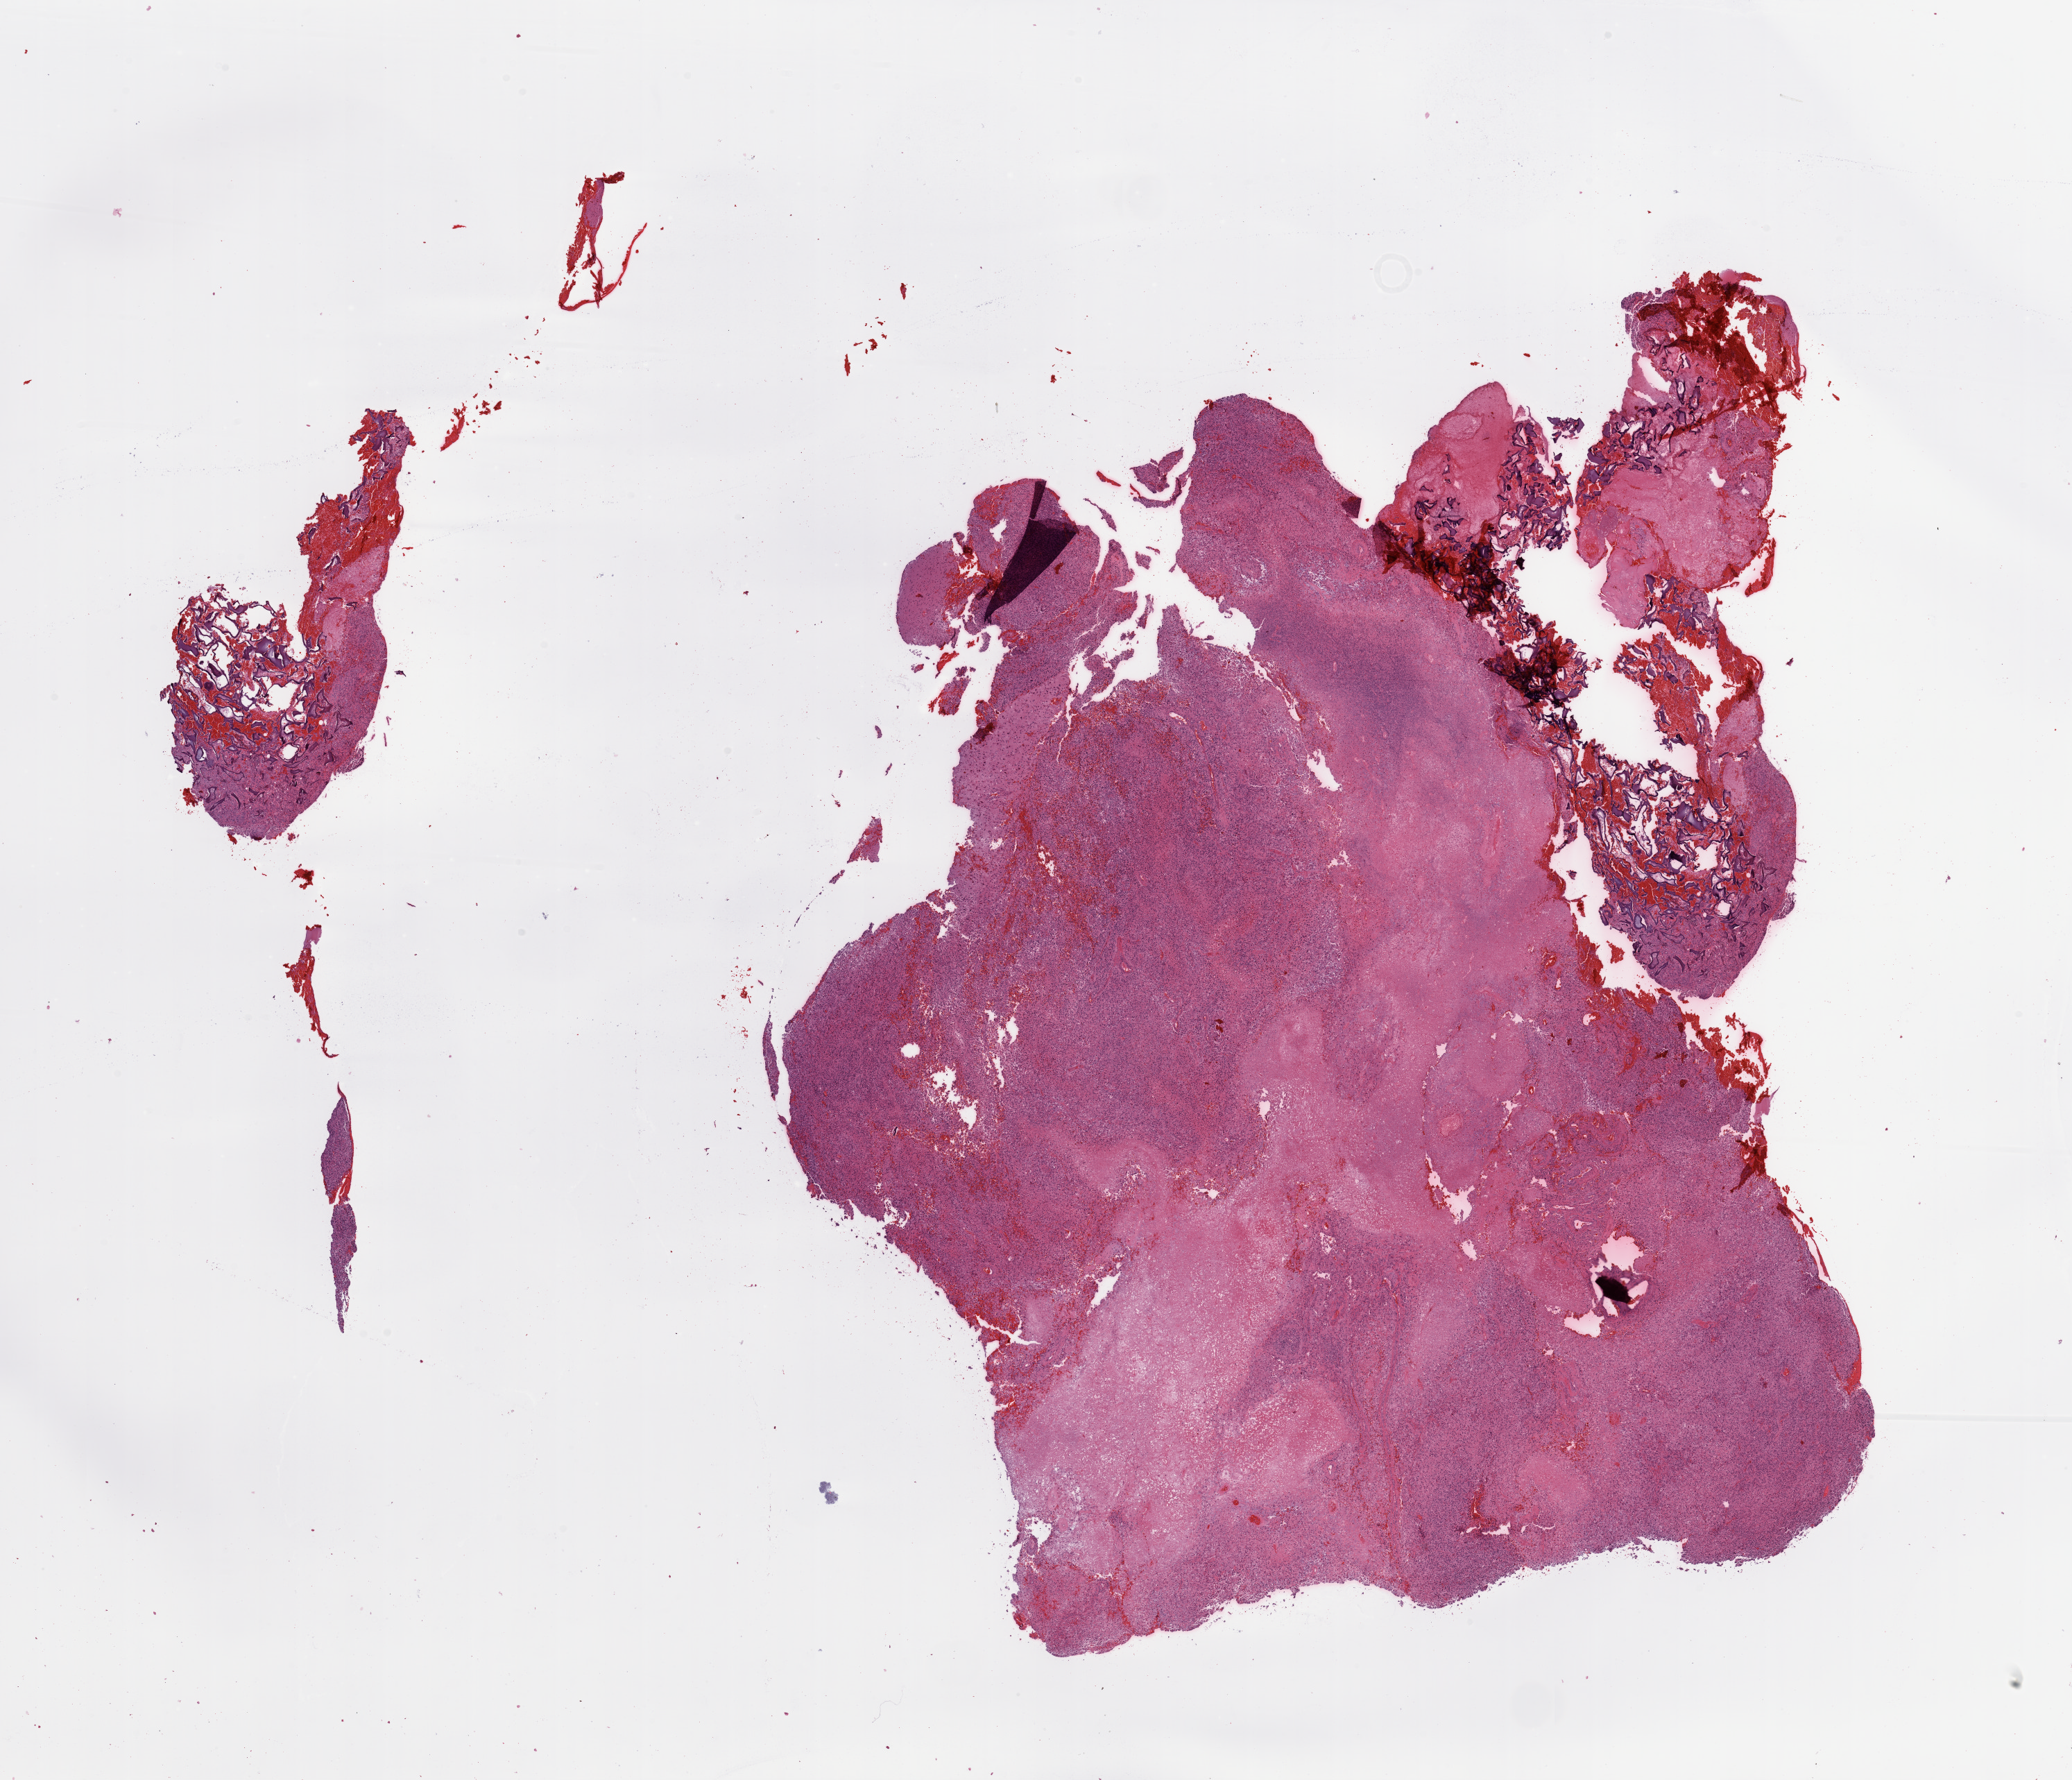
Hematoxylin and eosin (H&E) stained whole-slide image, low-resolution overview of the scanned area, about 23.6 x 20.3 mm (slide scanned at 20x), tumour tissue sample, sampled site: frontal lobe. Male, 60 y/o. Slide review estimates, as recorded: tumour nuclei 75%, necrosis 25%.
Diagnosis: Glioblastoma. Primary tumour site (as recorded): frontal lobe.